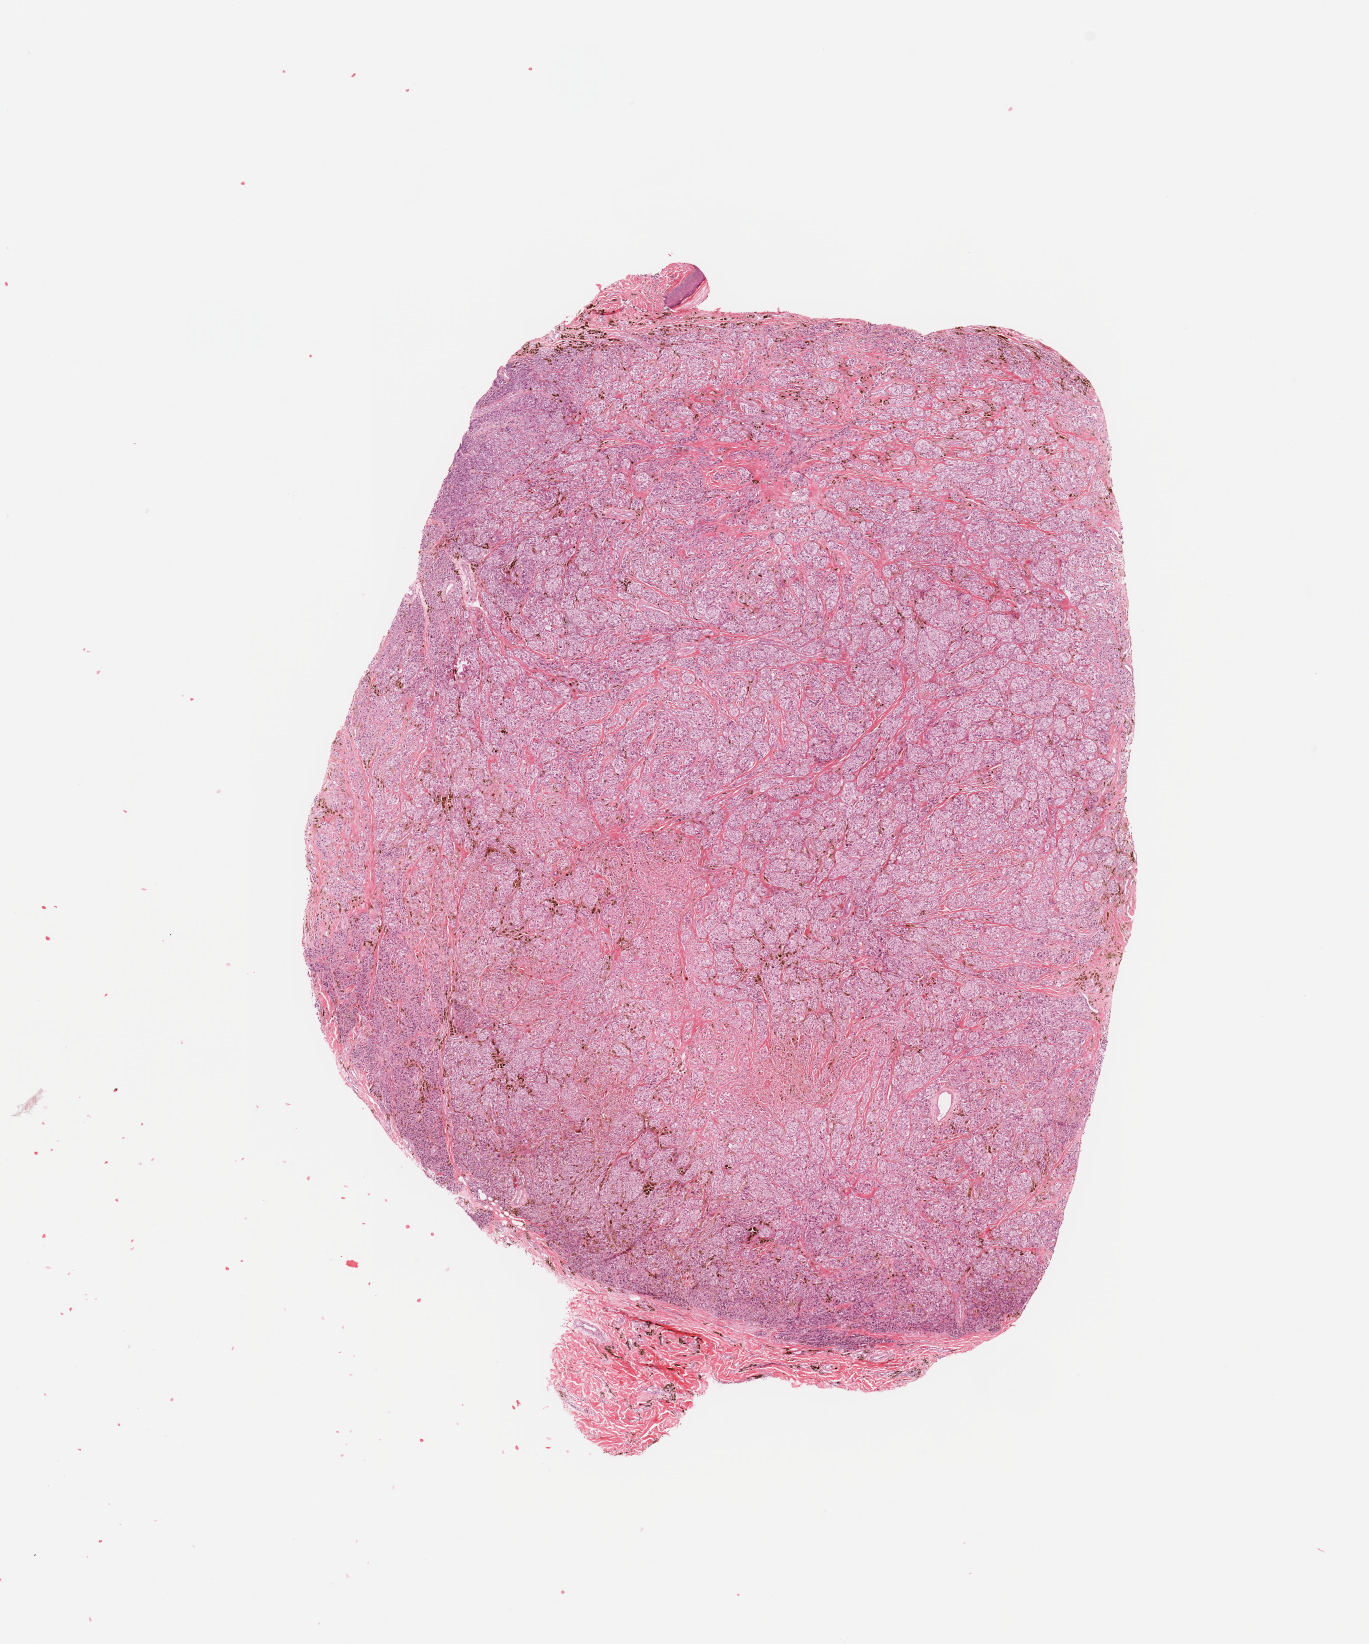
Whole-slide histology image, H&E, whole scanned area (about 10.8 x 13.0 mm, acquisition: 20x scan) shown as a low-resolution overview. Tumour tissue sample, sampled site: trunk. Patient: female, age 81 years. Slide review estimates, as recorded: tumour nuclei 90%, necrosis 0%.
Primary tumour site (as recorded): trunk. AJCC pathologic stage: IIC. Histologic diagnosis: Malignant melanoma, NOS.